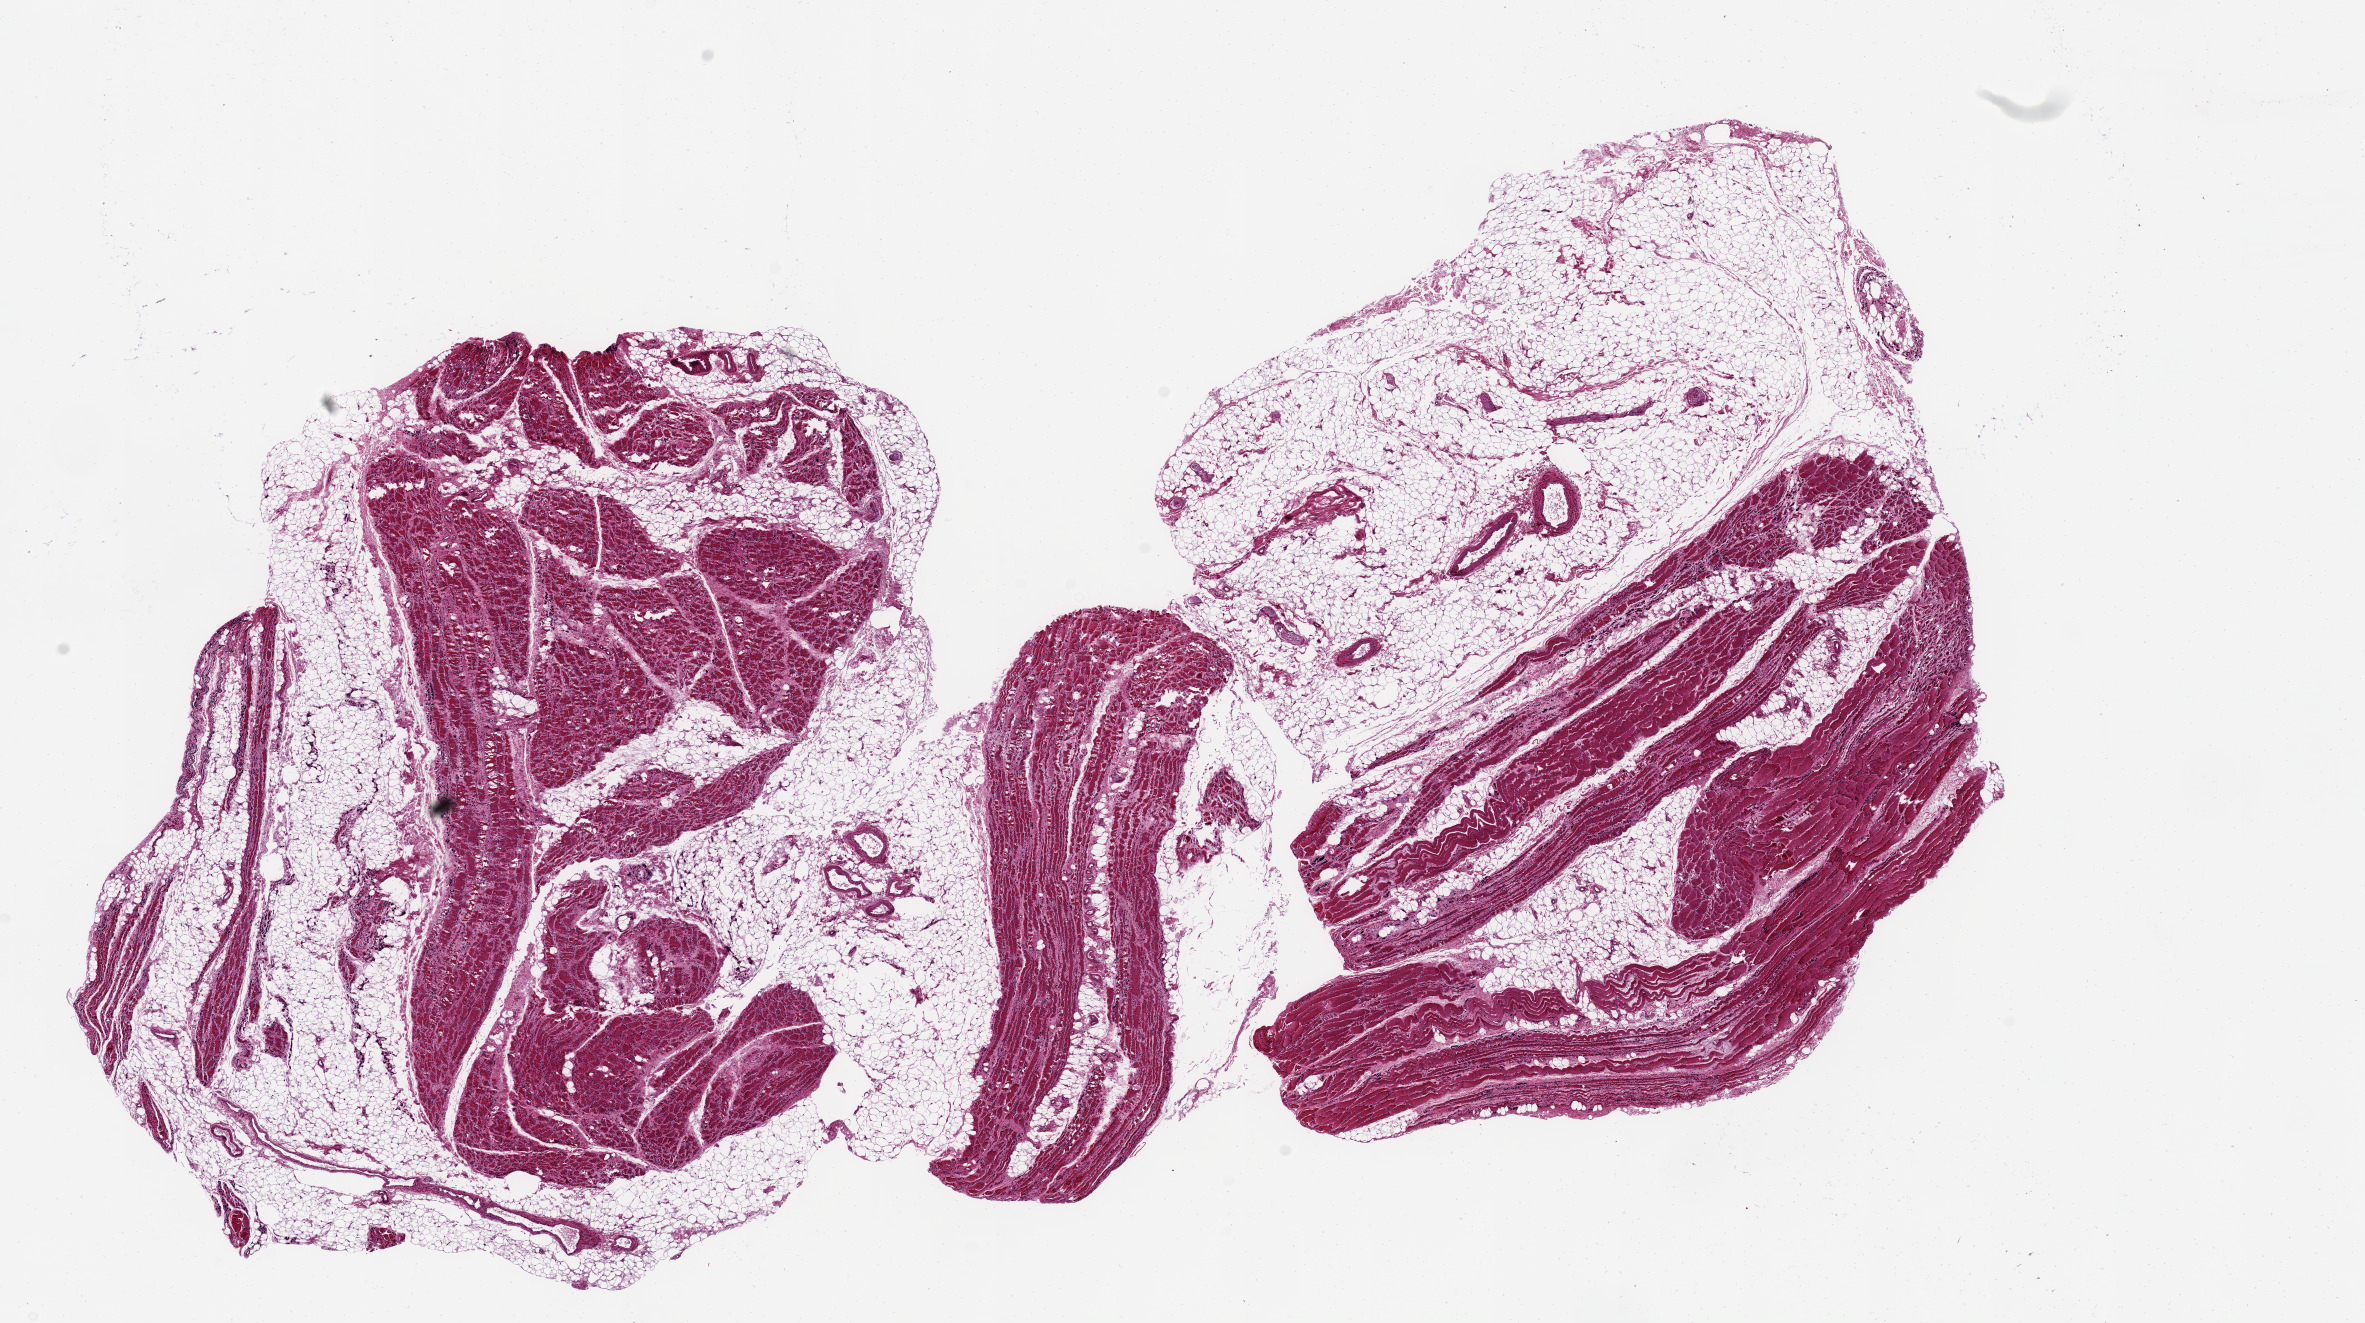
Haematoxylin and eosin whole-slide image, shown as a low-resolution overview of the whole scanned area (about 18.7 x 10.5 mm, slide scanned at 20x); PAXgene-fixed, paraffin-embedded tissue; section of skeletal muscle (target tissue); donor tissue sample. Donor sex: female.
Reviewer comment on this tissue sample: 2 ~8x7mm pieces, 50% fat. ? myositis/atrophic process. Withered muscle, fibrosis with fatty infiltration.